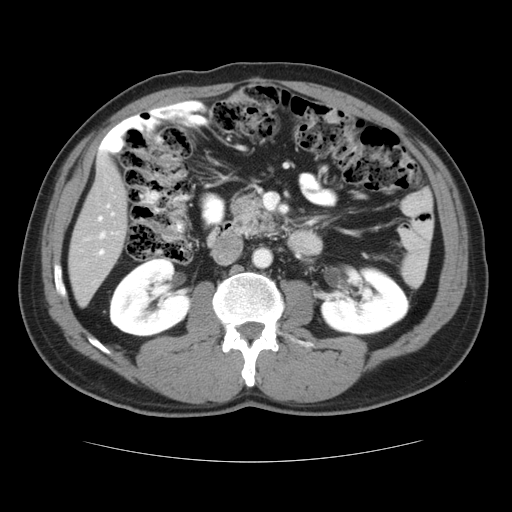
Contrast-enhanced abdominal CT, one axial slice. Intravenous contrast given. Soft-tissue window (W 400 / L 40 HU). 5 mm slice thickness. 512 × 512 image matrix, field of view 374 × 374 mm. Male patient, age 66 years. From the clinical record (not read from this slice): diagnosis: colorectal cancer liver metastases, imaged before liver resection; multiple liver metastases: yes; largest metastasis: 1.6 cm; chemotherapy before resection: no.
Outlined on this slice (expert manual segmentation):
- hepatic veins: bounding box (x1, y1, x2, y2) in pixels: (98, 204, 115, 240)
- liver: (70, 154, 128, 306)
- planned liver remnant (the part of the liver to remain after resection): (70, 180, 127, 305)
- portal vein (with intrahepatic branches): (99, 217, 104, 255)